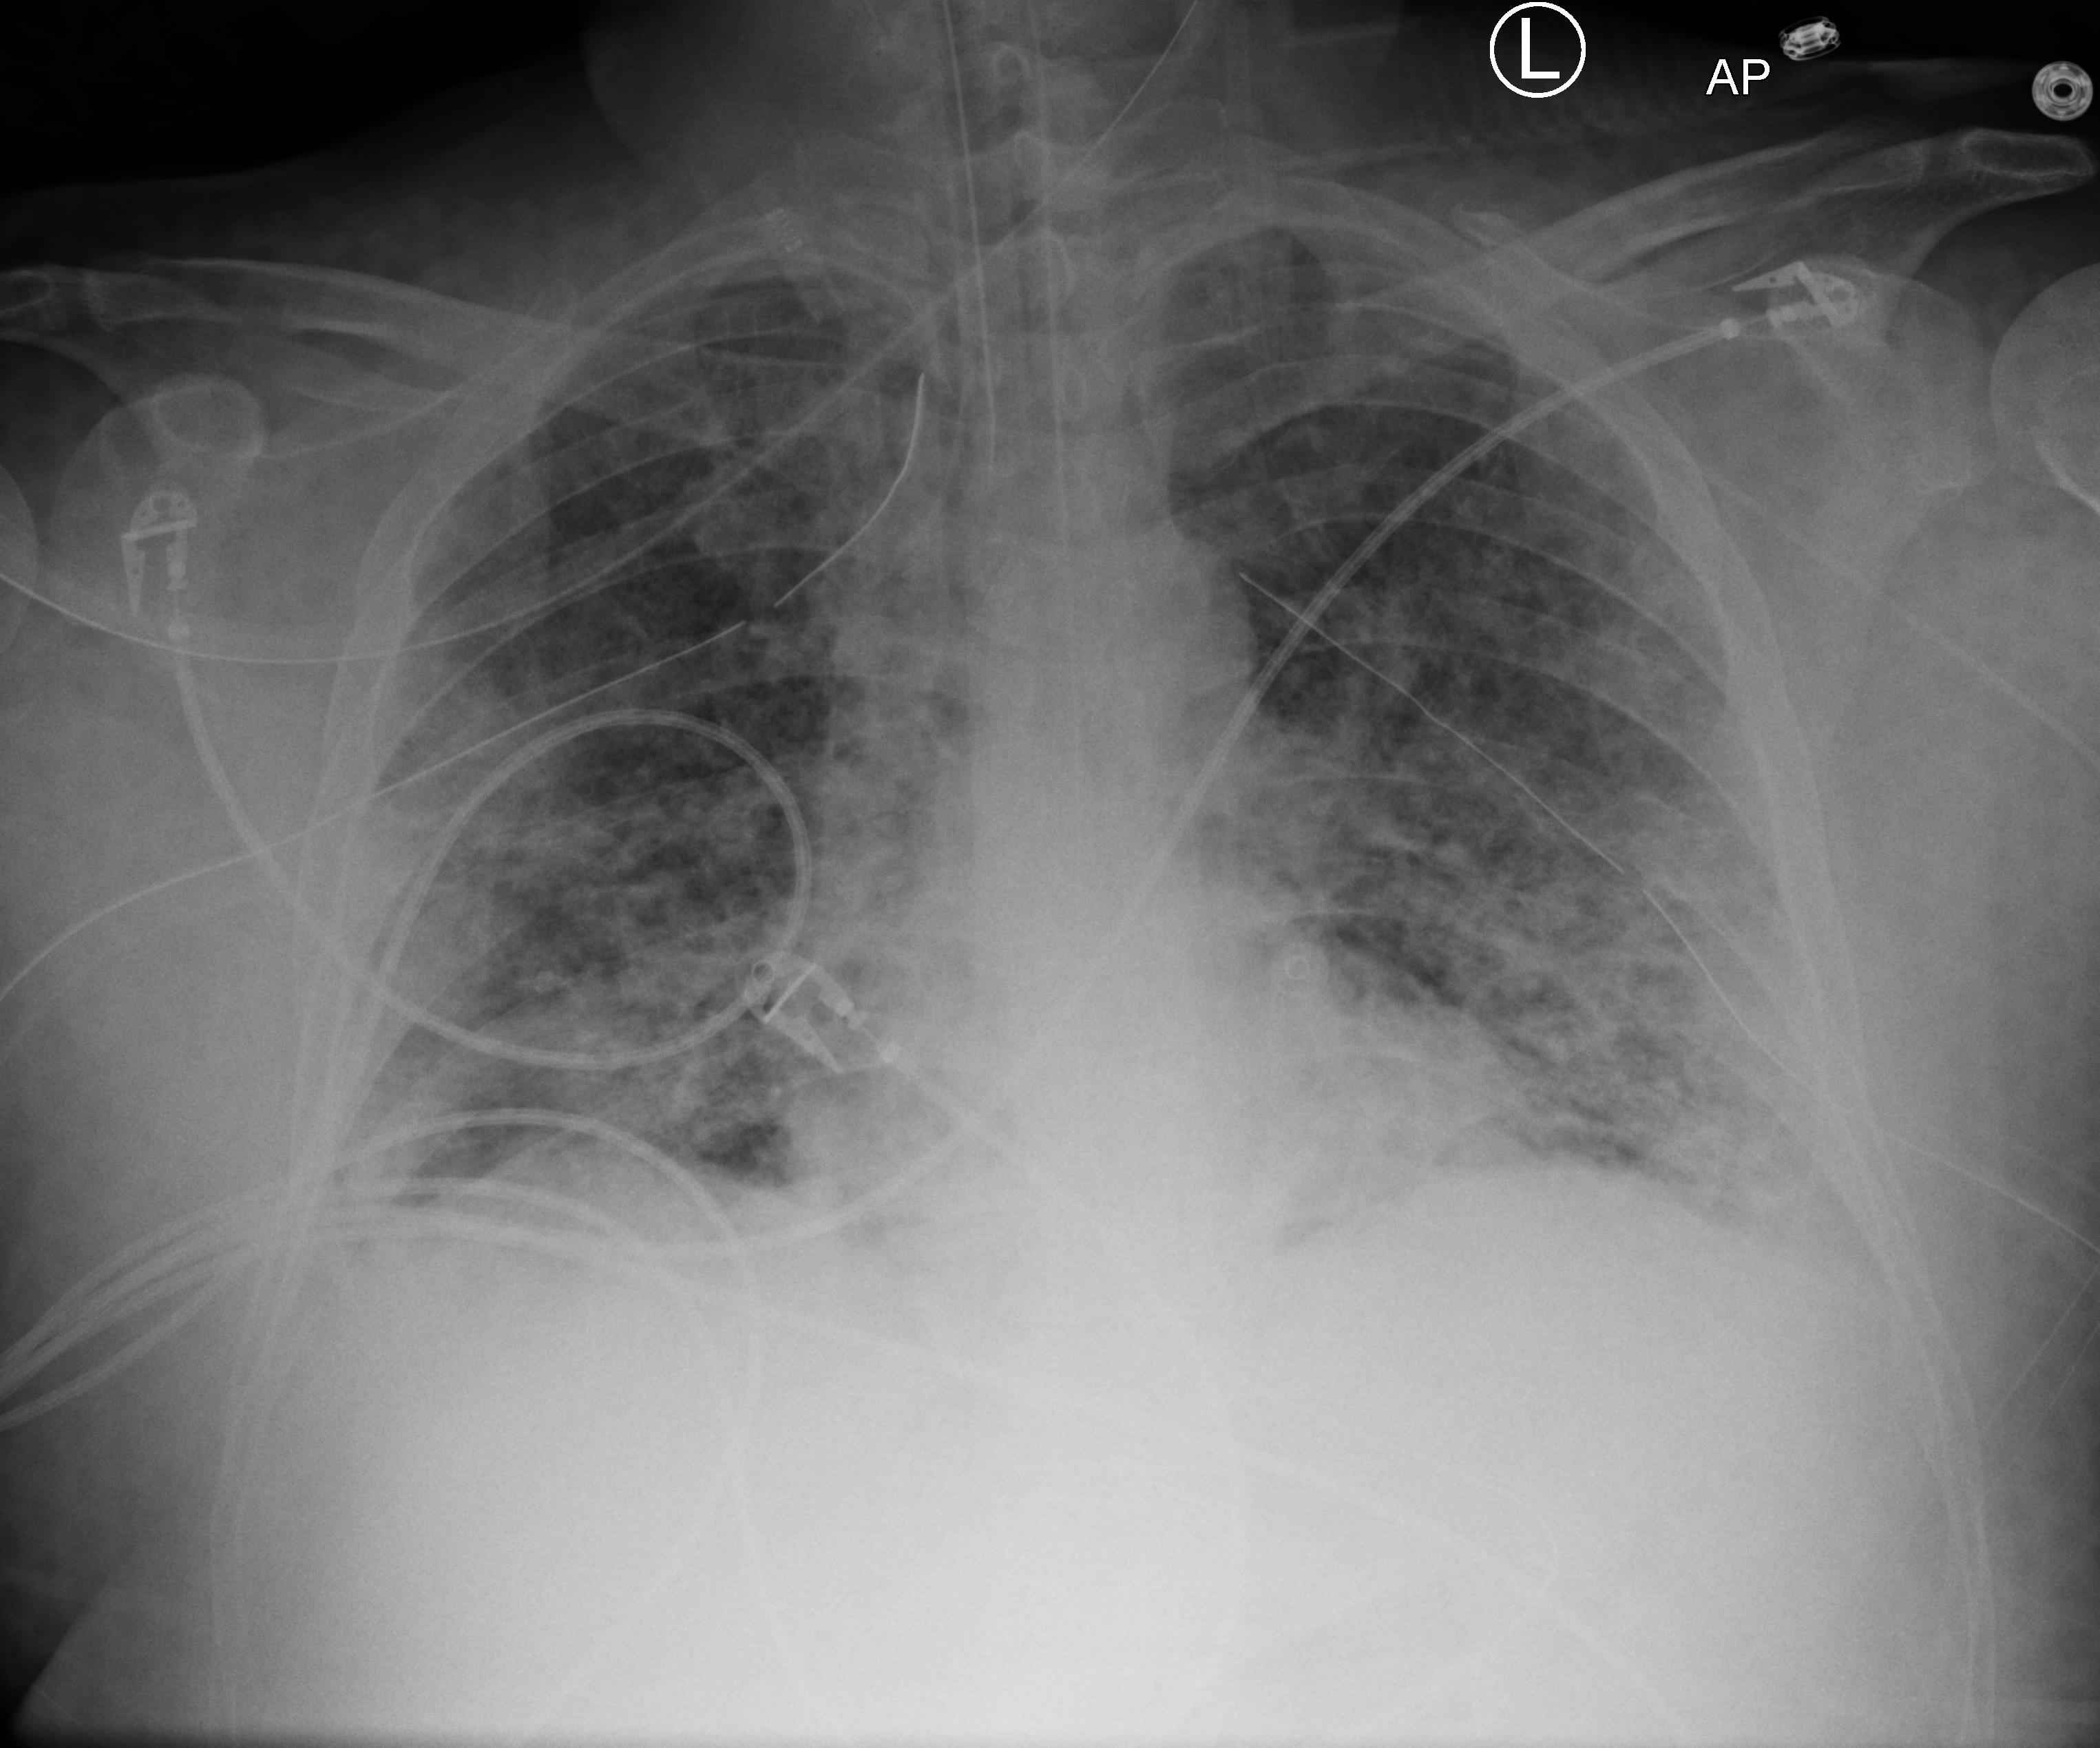
Bedside chest radiograph (computed radiography). Male patient hospitalised with COVID-19, age 18–59 years.
Admission-level facts for this patient (not findings on this image; timing relative to this image not recorded):
- admitted to intensive care during this hospital stay: yes
- mechanically ventilated during this hospital stay: yes
- hypertension (admission record): yes